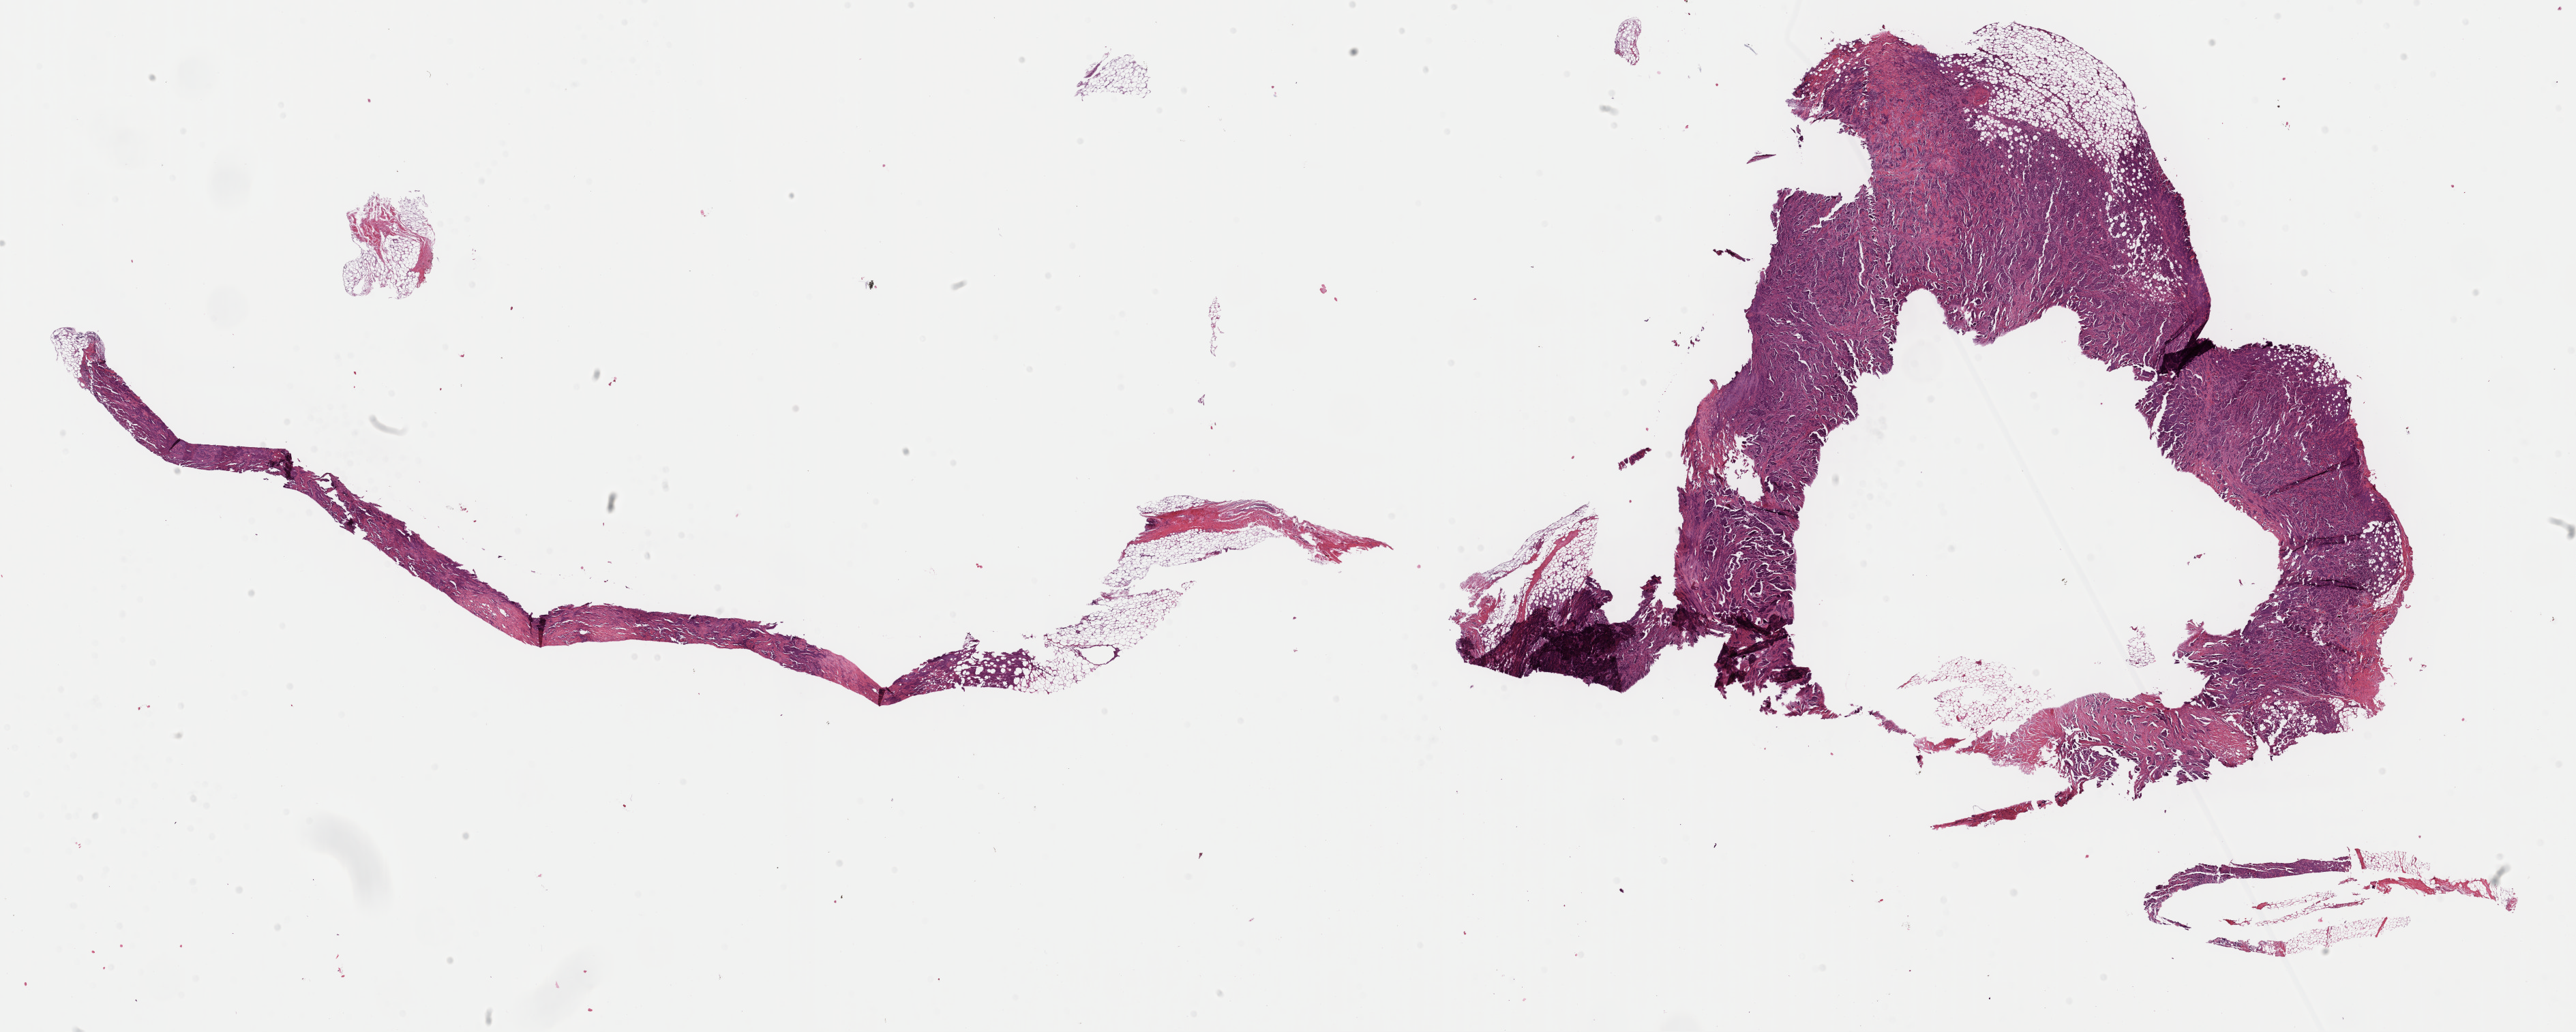
Digitized H&E tissue section (whole slide) — shown as a low-resolution overview of the whole scanned area (about 29.8 x 12.0 mm, from a 40x scan). FFPE section. Breast, primary tumour sample. Female, age 46 years at initial diagnosis.
Pathologic diagnosis: Infiltrating duct carcinoma, NOS. AJCC pathologic stage: IIA (6th edition). Laterality: right.